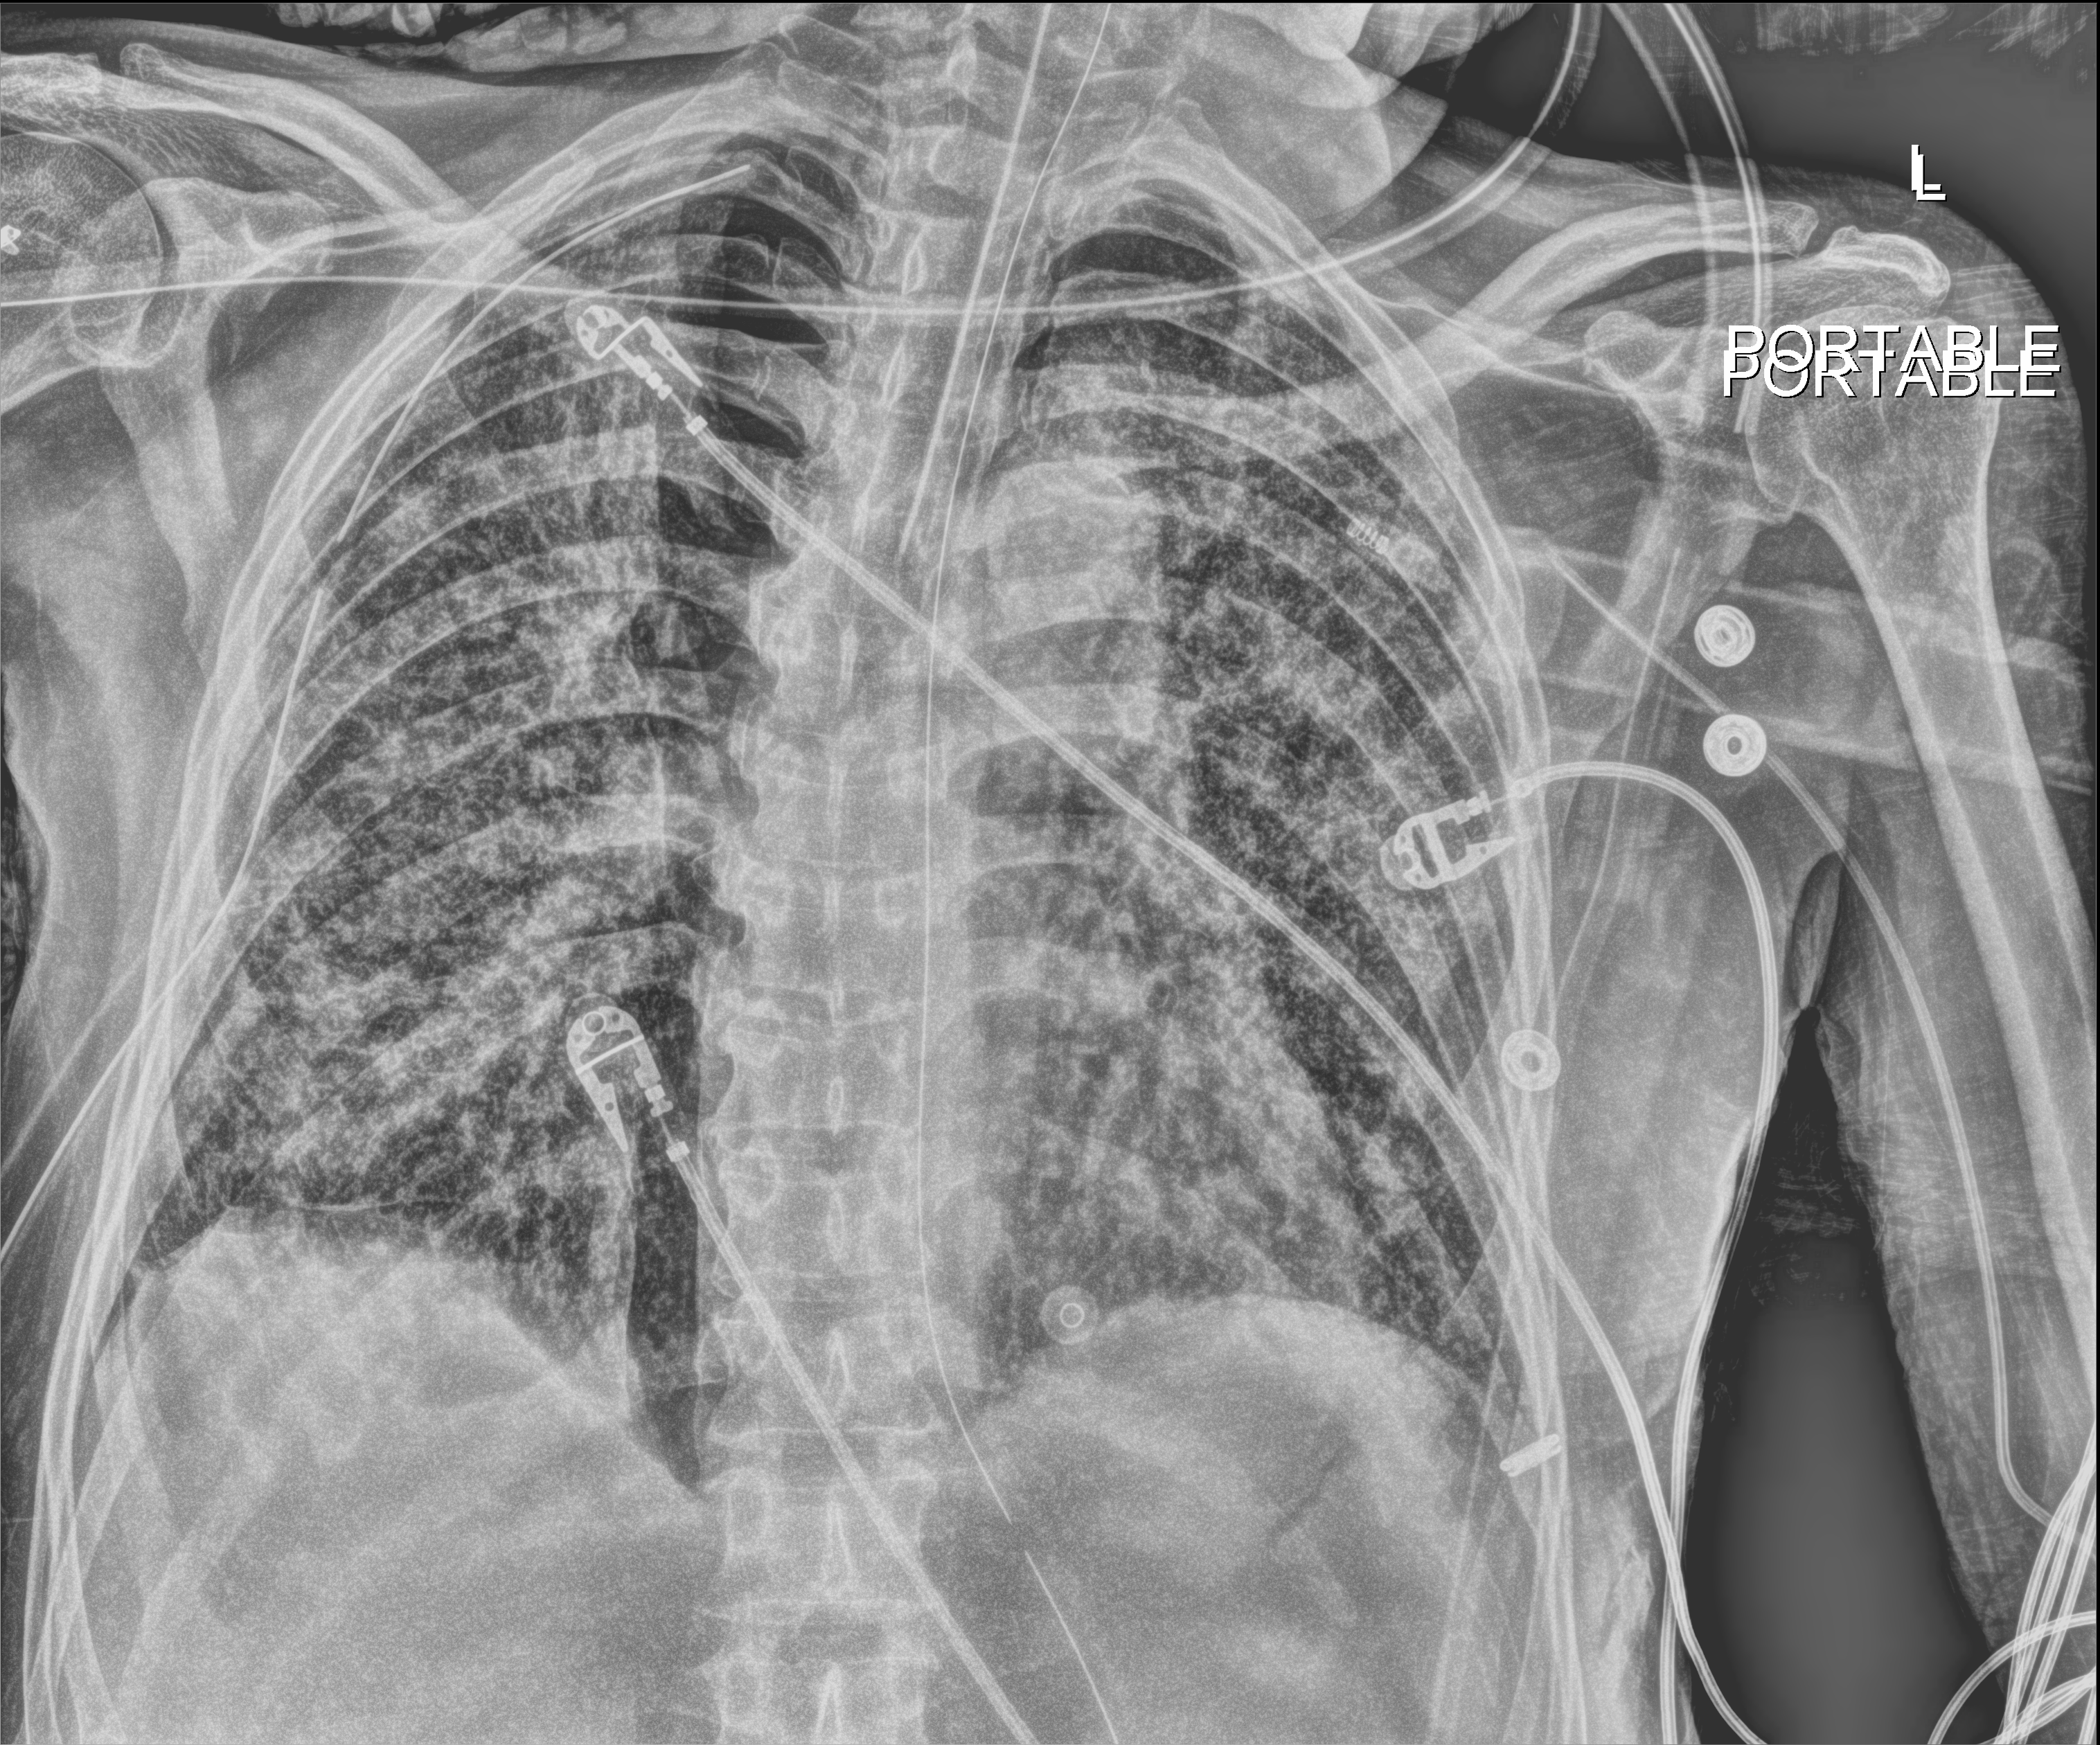
Chest X-ray (portable), anteroposterior (AP) projection. Patient hospitalised with COVID-19; male, aged 60–74 years.
Hospital-stay facts (about this admission, not read from this image; timing relative to this image not recorded):
- admitted to intensive care during this hospital stay: yes
- smoking status (admission record): never